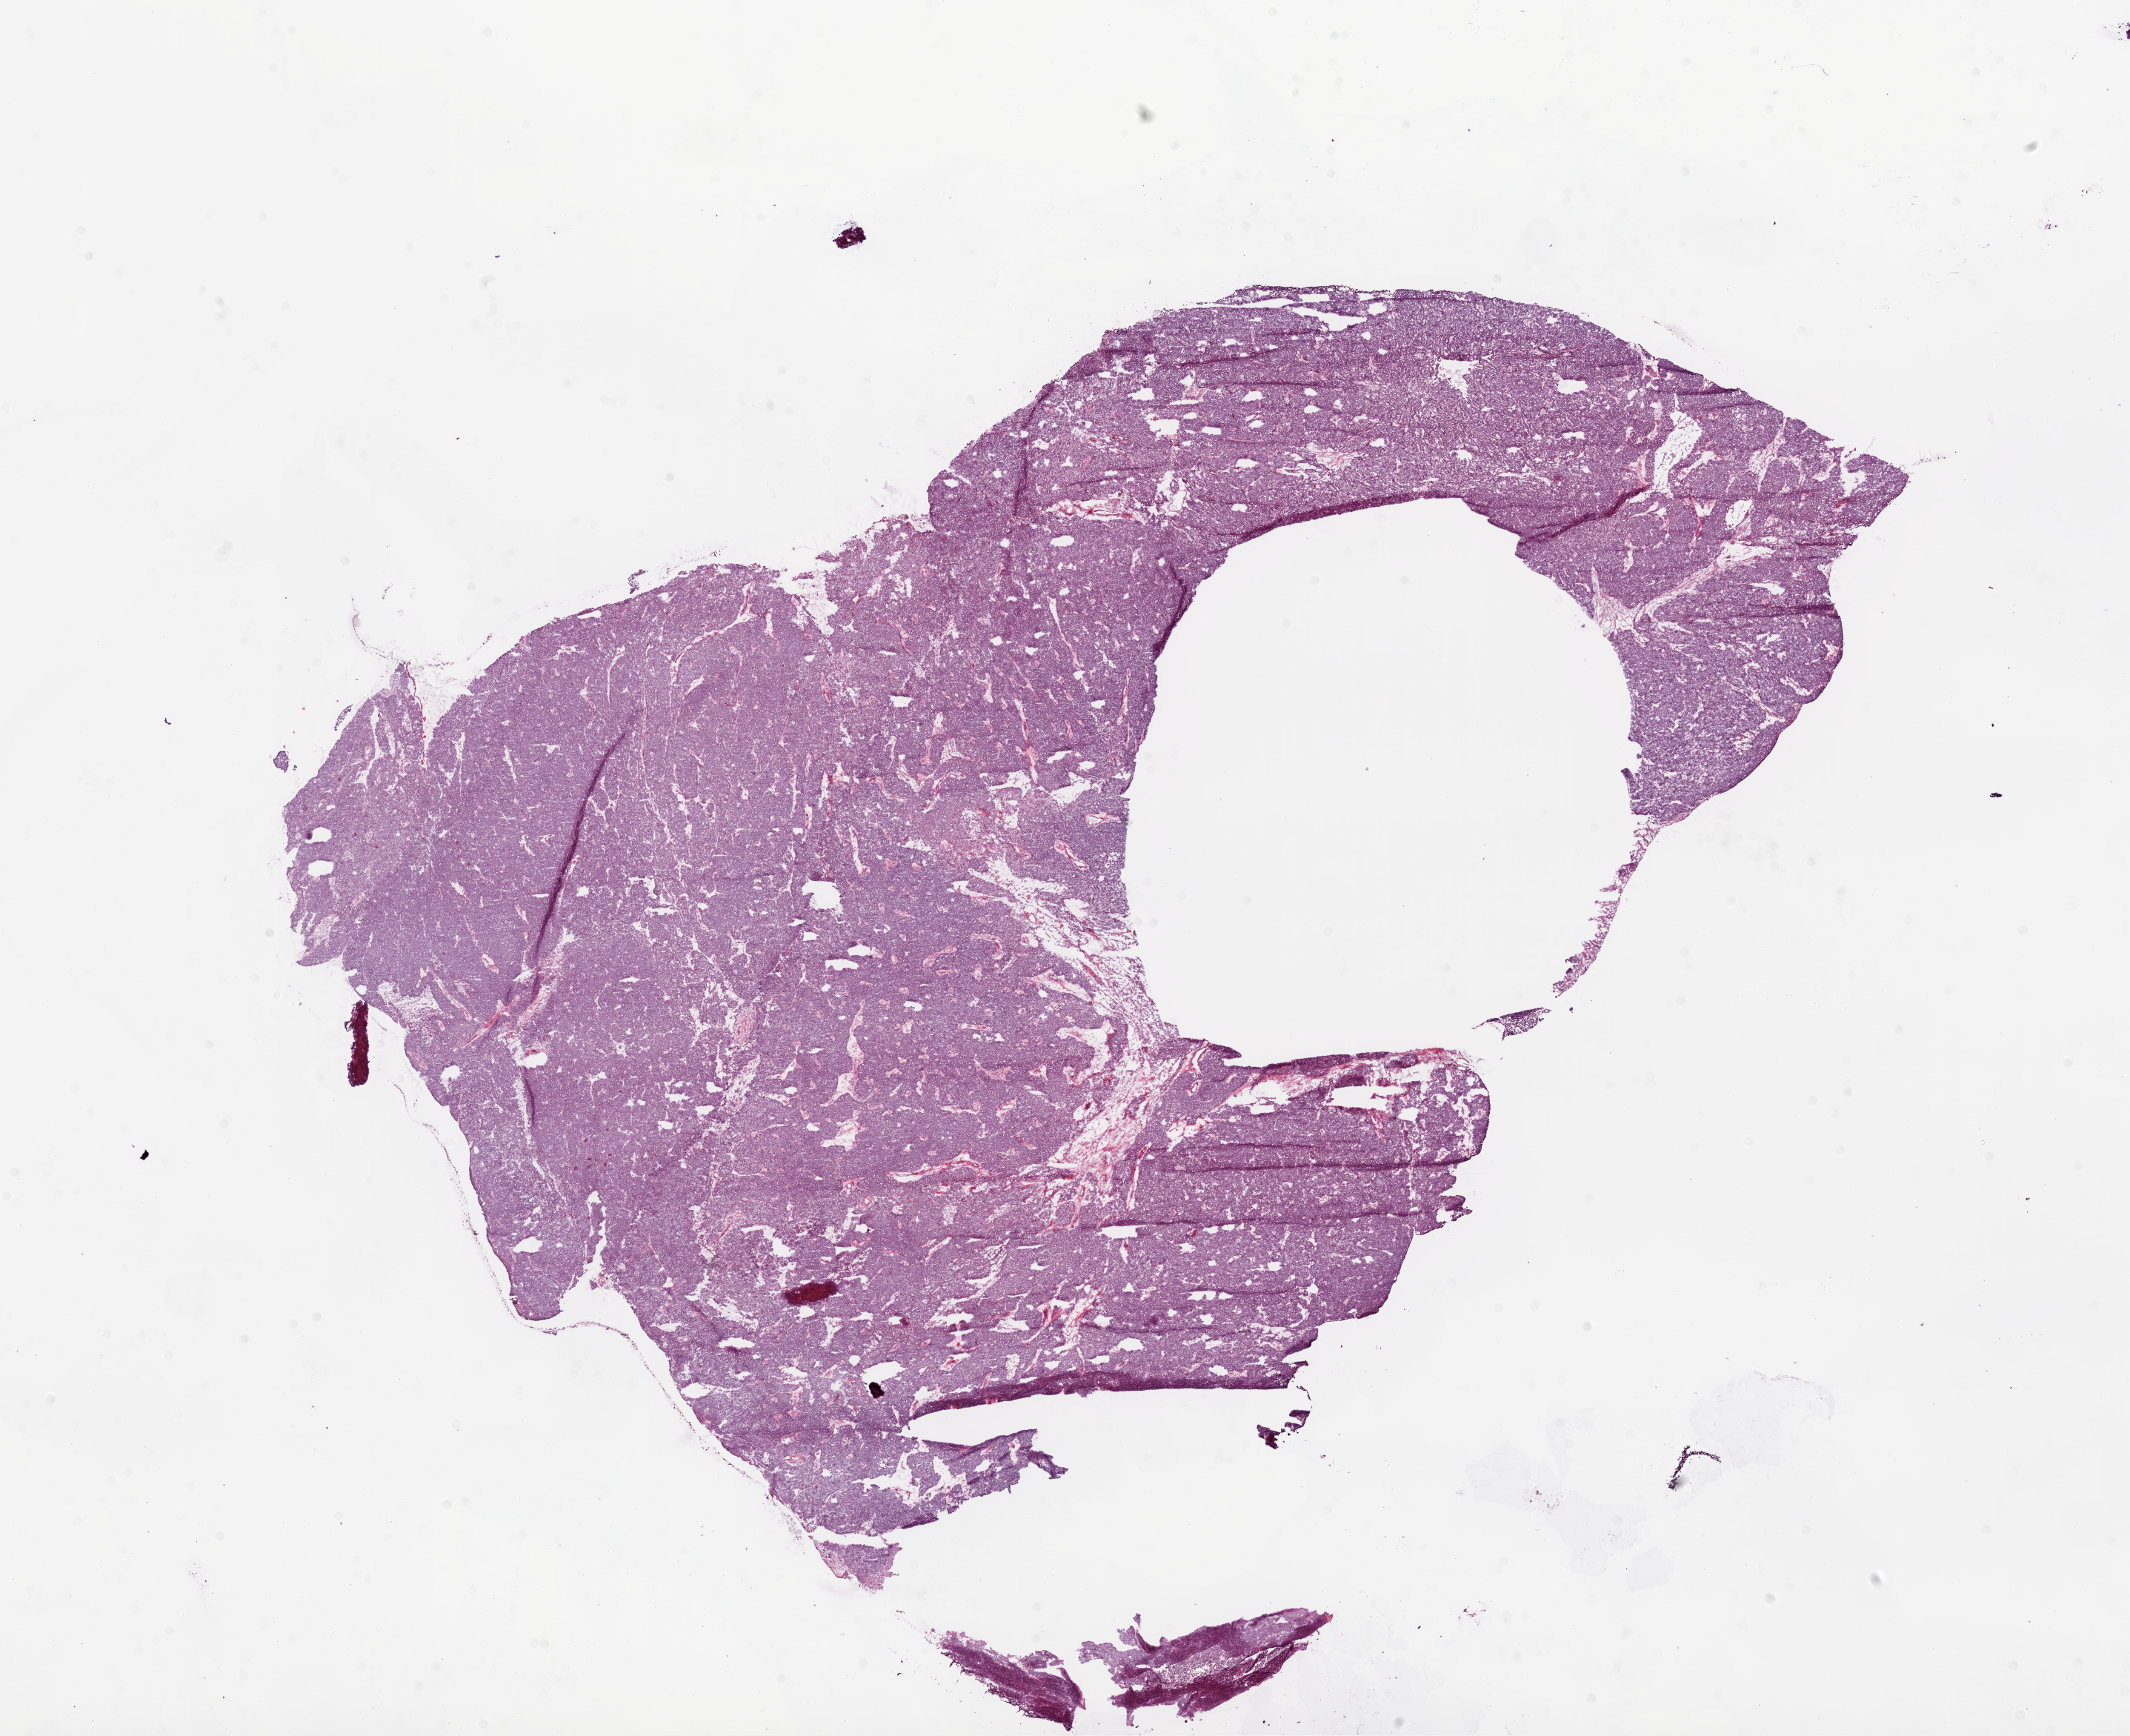
H&E-stained whole-slide image, whole scanned area (about 23.1 x 18.8 mm) shown as a low-resolution overview, frozen section from the bottom of the tissue portion, ovary, primary tumour sample. Female, age 56 years at initial diagnosis. Histologic grade: G3 (poorly differentiated). Pathologist review of this section (percent, as recorded): tumour cells 94%, tumour nuclei 95%, normal cells 0%, stromal cells 5%, necrosis 1%.
- histologic diagnosis: Serous cystadenocarcinoma, NOS
- FIGO stage: IIC